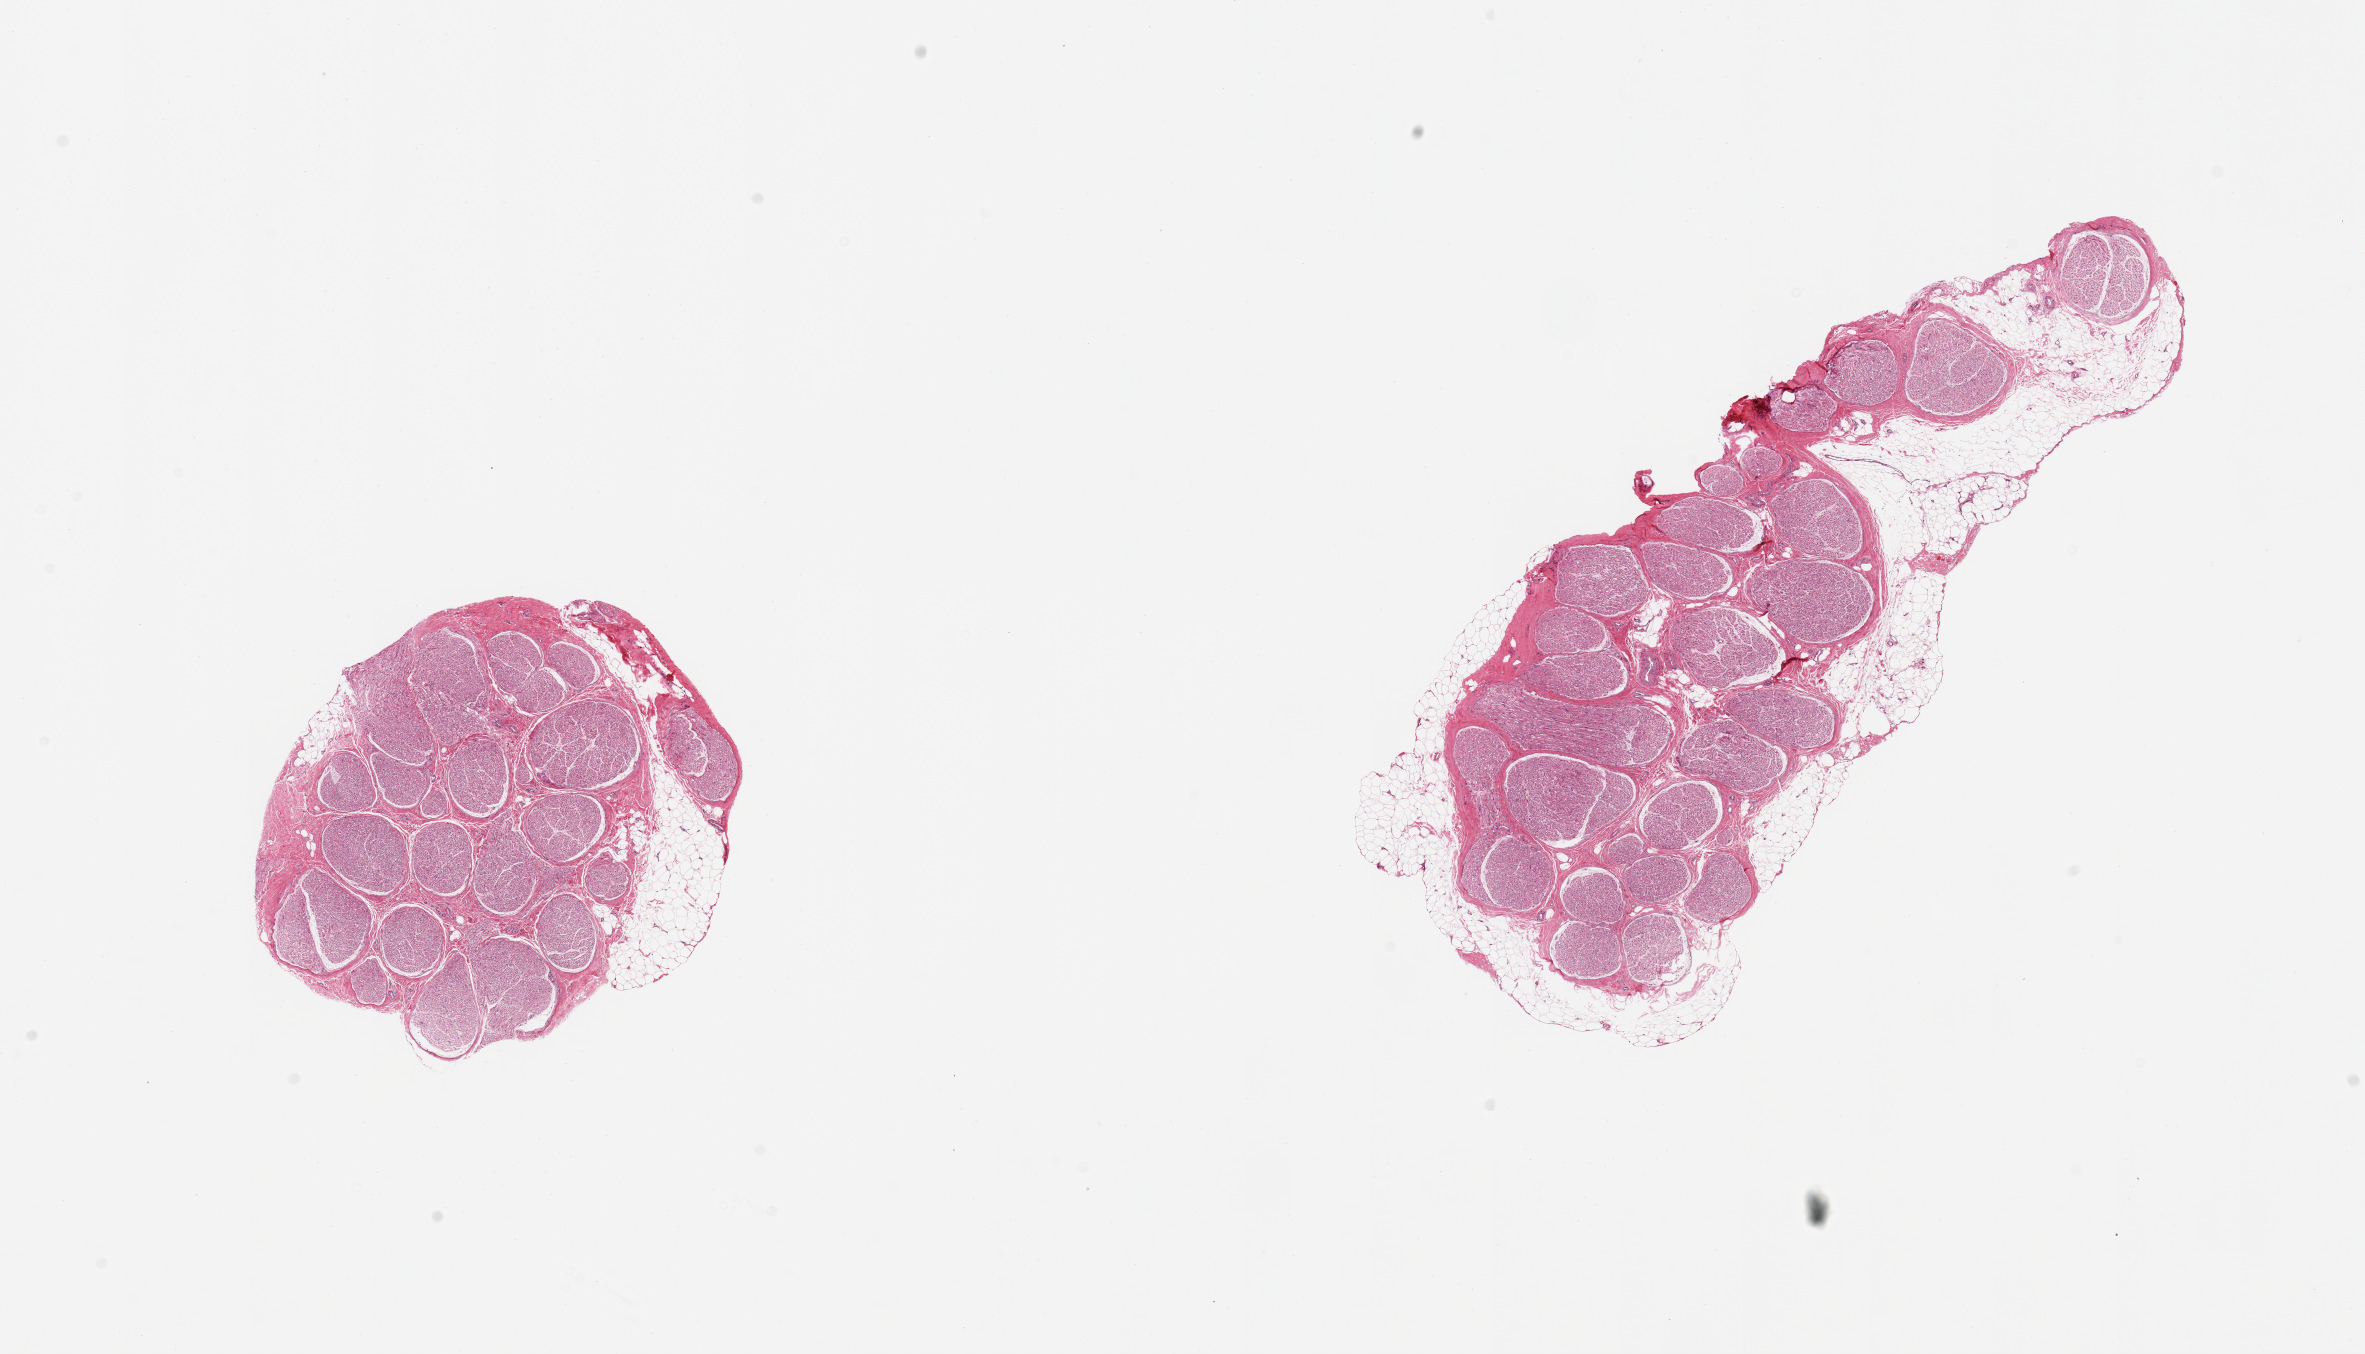
H&E whole-slide image — low-resolution overview of the scanned area, about 18.7 x 10.7 mm (from a 20x scan), PAXgene-fixed, paraffin-embedded tissue, sampled site (target tissue): tibial nerve, tissue donor sample. Male donor.
Pathologist's review note for this sample: 2 pieces; small piece includes ~10% fat, larger piece includes nearly circumferential rim of fat up to 40%.